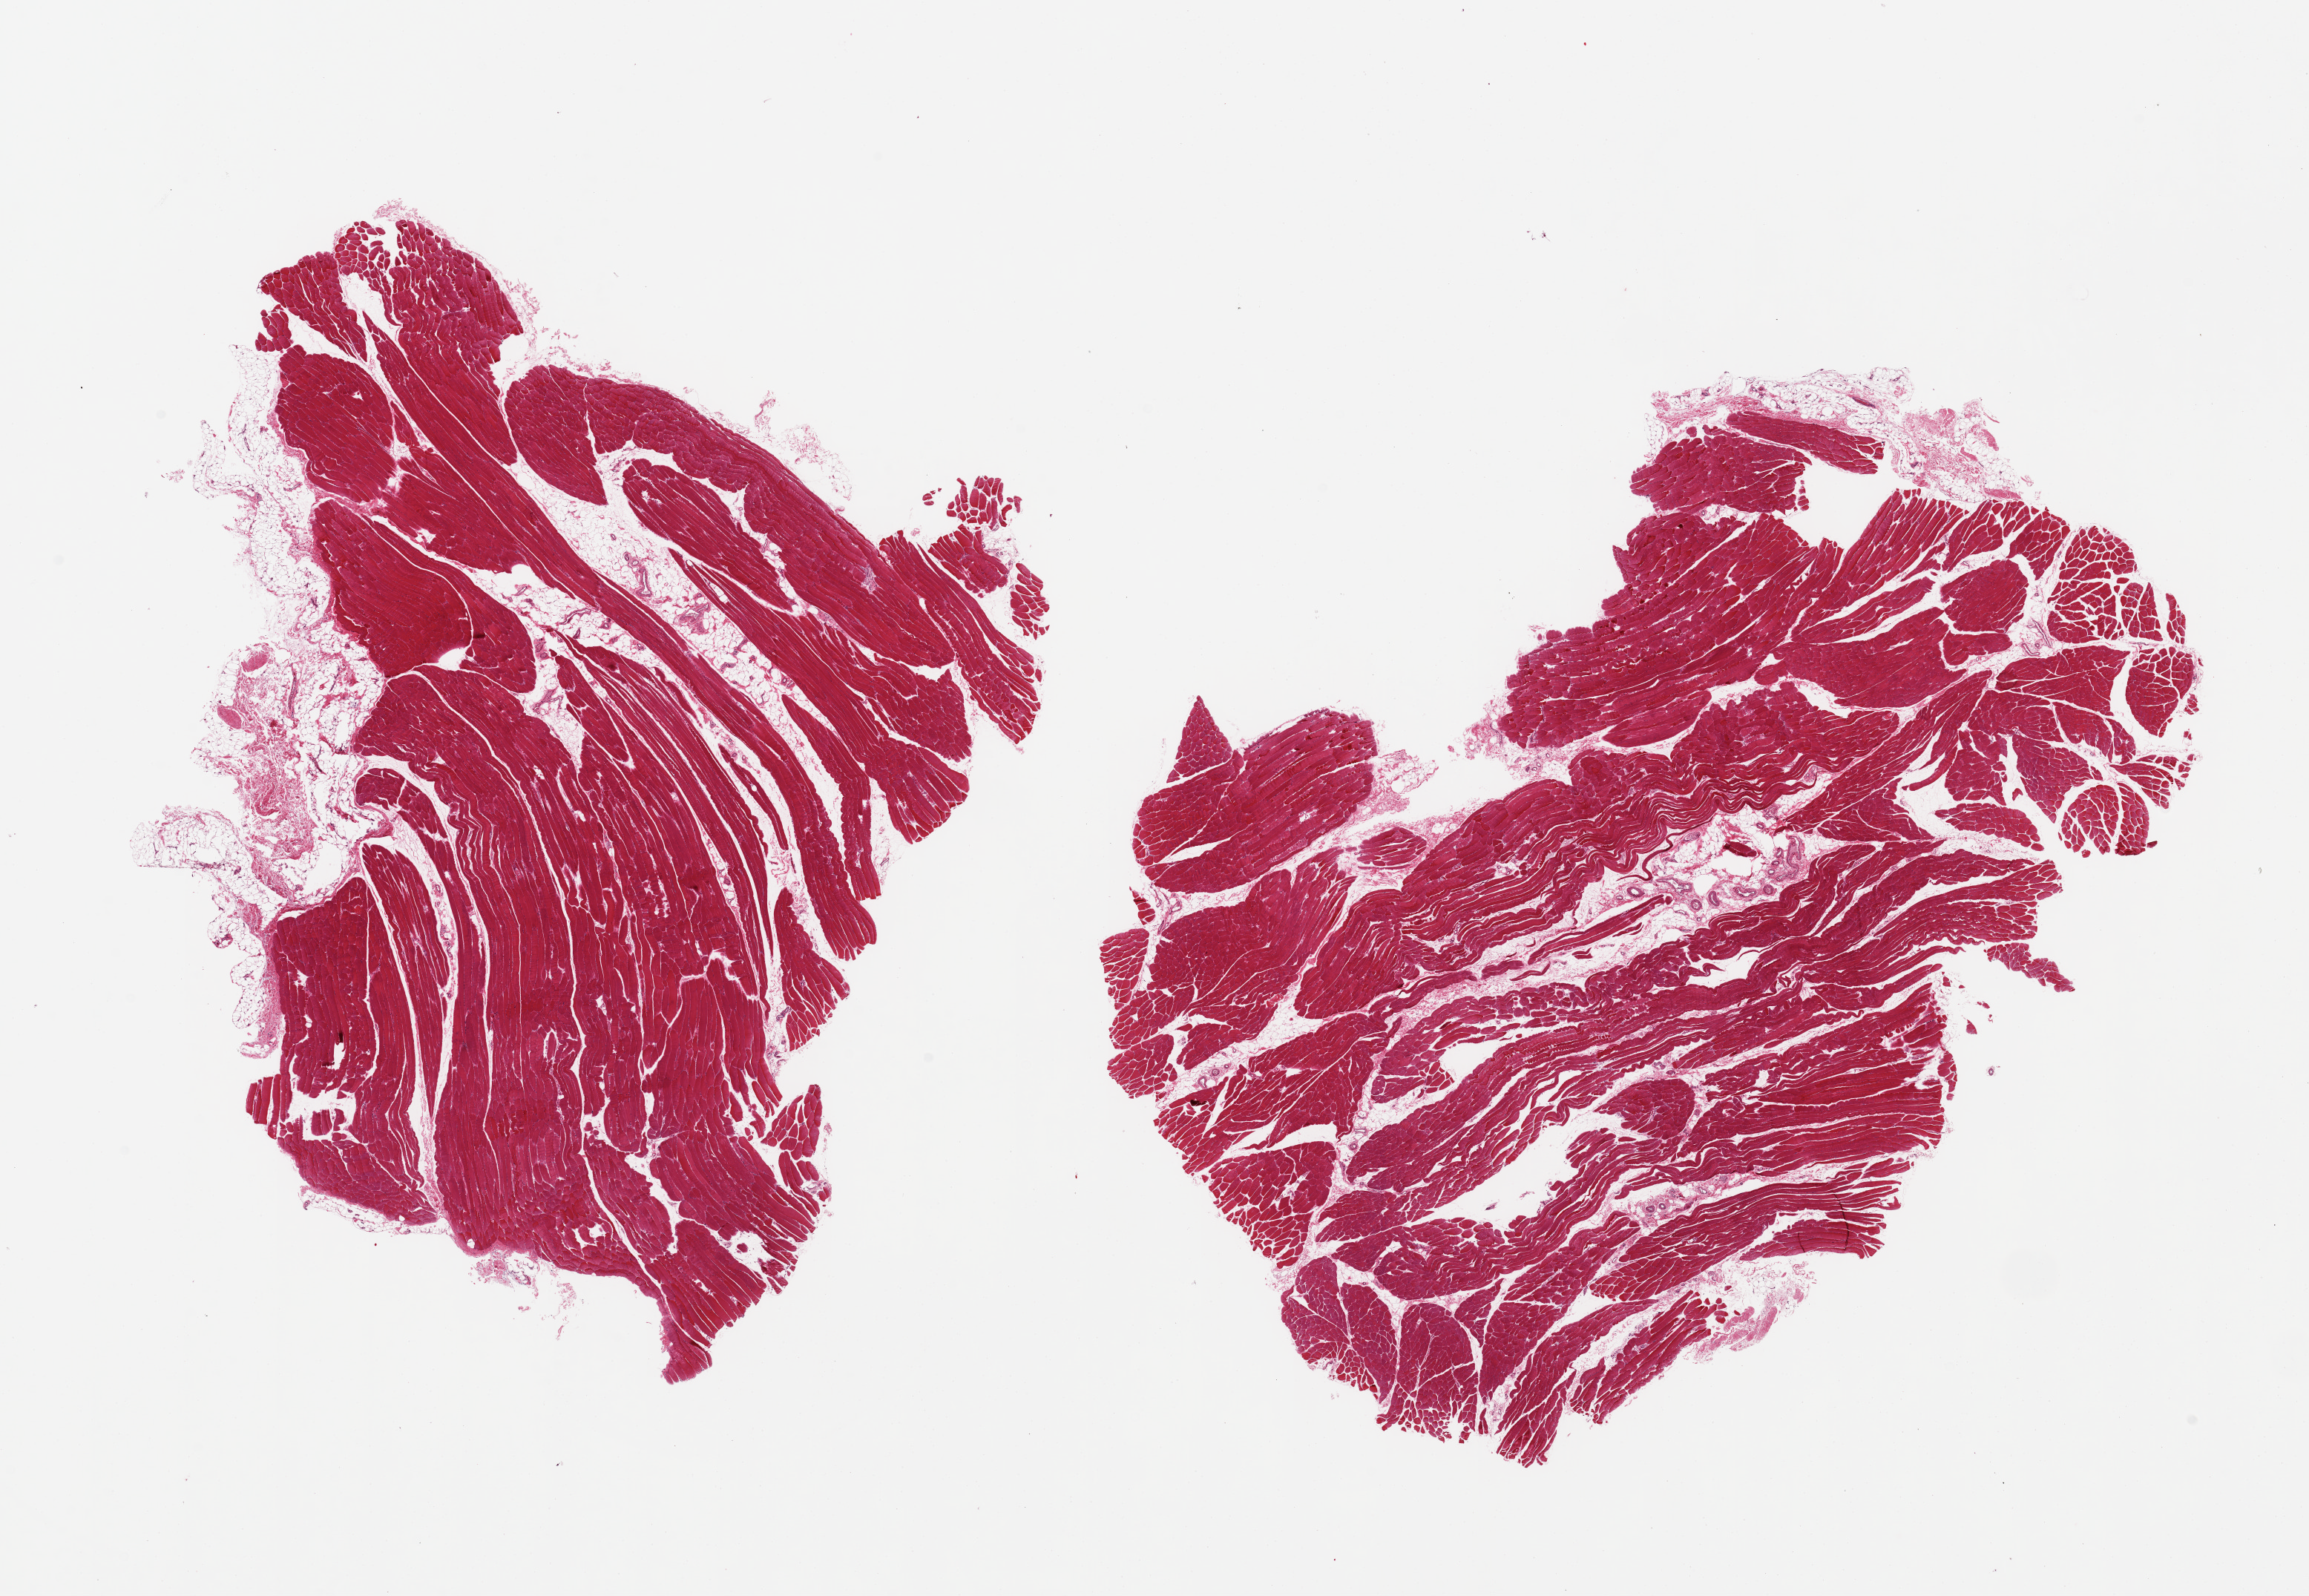
Digitized H&E-stained section, brightfield — a low-resolution overview of the entire scanned area, about 24.6 x 17.0 mm; PAXgene-fixed, paraffin-embedded tissue; section of skeletal muscle (target tissue); tissue donor sample.
* pathologist's review note for this sample: 2 pieces, 5-10% attached and internal adipose tissue